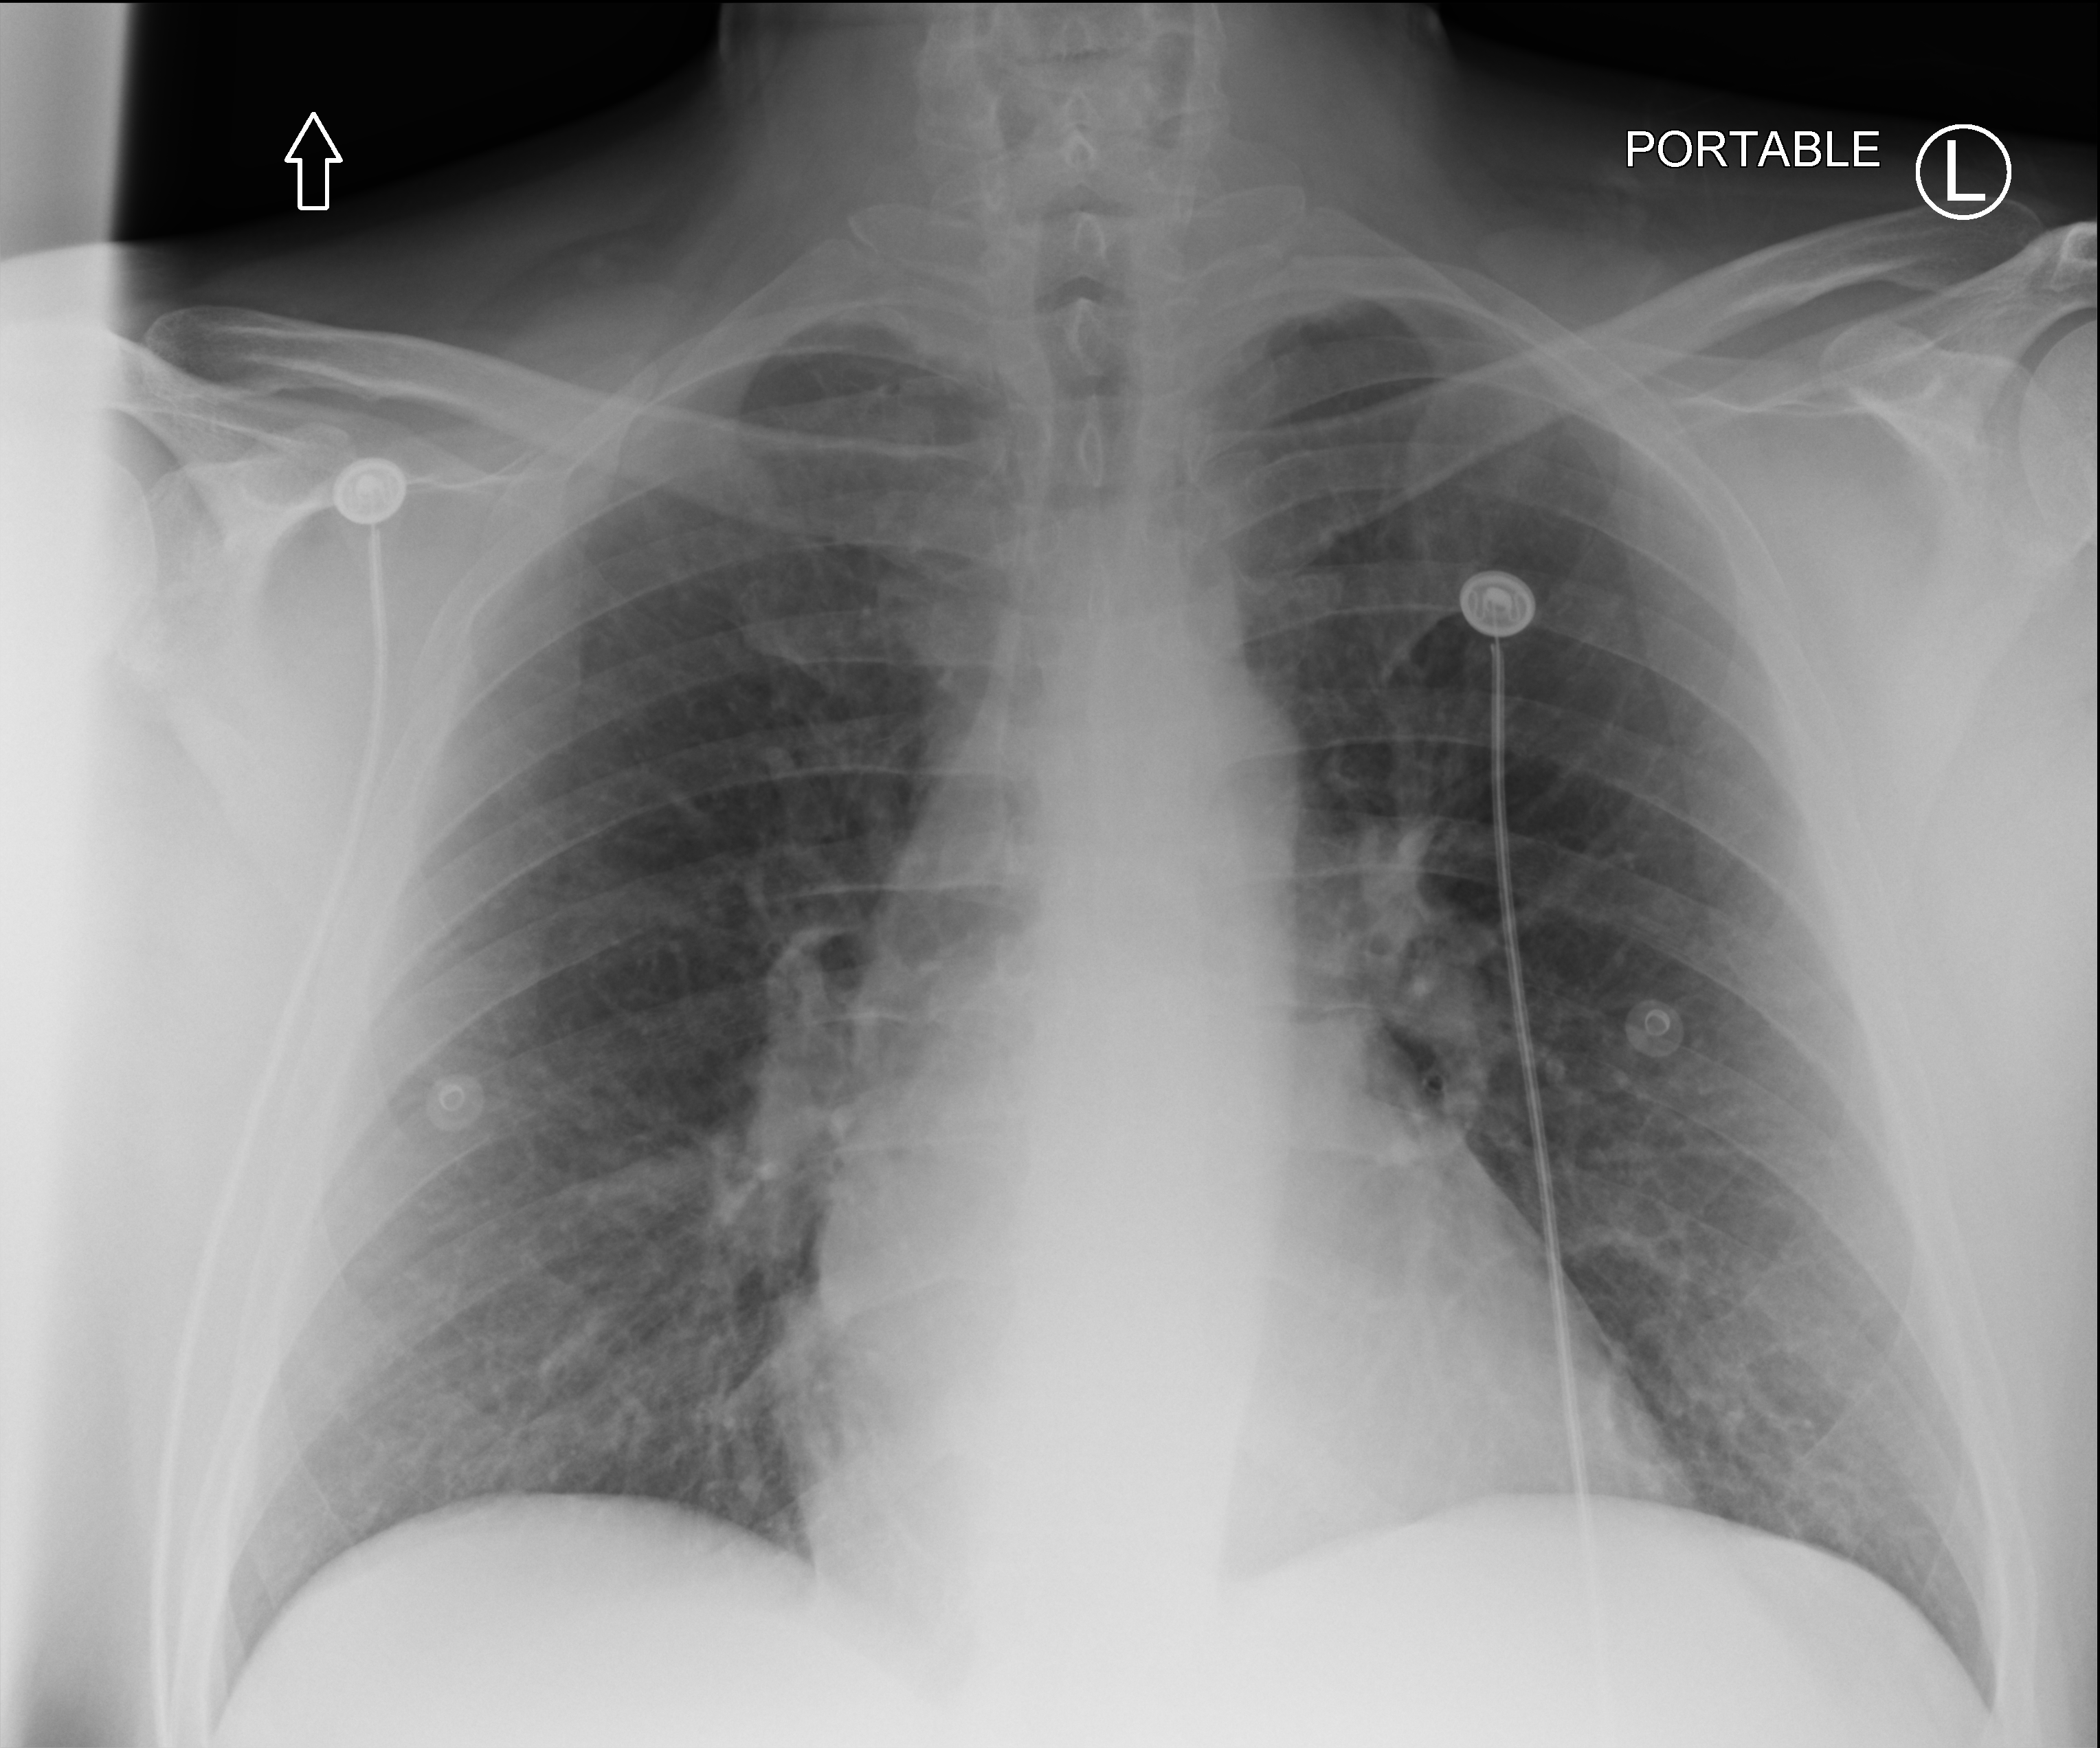
Chest X-ray (portable), anteroposterior (AP) projection. Patient hospitalised with COVID-19; male, aged 18–59 years.
Admission-level facts for this patient (not findings on this image; timing relative to this image not recorded): COPD (admission record): no; mechanically ventilated during this hospital stay: no.